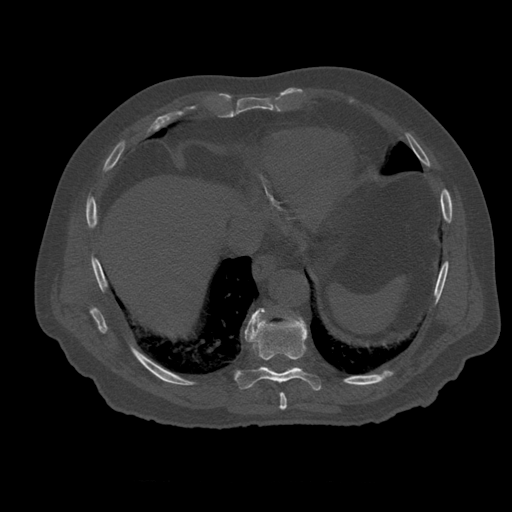
CT including the spine, one axial slice; position 321 of 399 along the scan axis; reconstruction kernel STANDARD; bone window (W 1800 / L 400 HU); 1.25 mm slice thickness; 512 × 512 image matrix, field of view 407 × 407 mm. Patient age 73 years. Case-level facts recorded for this patient, not image findings: primary cancer: prostate; vertebrae with lytic lesions (as recorded): L2.
Outlined on this slice (semi-automatically segmented with operator editing):
- T10 vertebra: bounding box (x1, y1, x2, y2) in pixels: (292, 320, 296, 322)
- T8 vertebra: (280, 393, 287, 411)
- T9 vertebra: (235, 308, 322, 391)